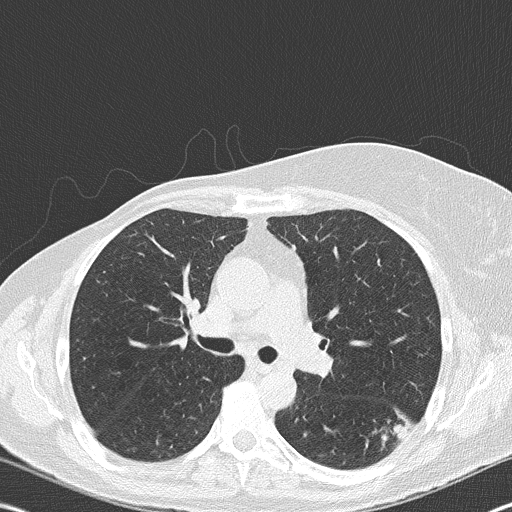
Low-dose screening chest CT, one axial slice; slice 113 of 177 in the series (ordered by position); reconstruction kernel B50f; lung window (W 1500 / L -600 HU); 2 mm slice thickness; 512 × 512 image matrix, field of view 342 × 342 mm.
Structures marked on this image (outlined manually by an expert reader):
- lesion 1 (tumor): bounding box [x1, y1, x2, y2] px = [389, 417, 411, 440]